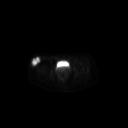
FDG PET of an extremity soft-tissue mass (from a PET/CT study), one axial slice; slice 65 of 267 in the series (ordered by position); 128 × 128 image matrix, field of view 700 × 700 mm. Patient: female, 34 years. From the clinical record (not read from this slice): histological type: synovial sarcoma; grade: intermediate; site of the primary tumour: right thigh.
Outlined on this slice (expert contour drawn on MRI and transferred to this co-registered scan by the dataset authors):
- gross tumour volume including surrounding oedema: bounding box [x1, y1, x2, y2] px = [30, 56, 40, 68]
- gross tumour volume (mass): [30, 56, 40, 67]